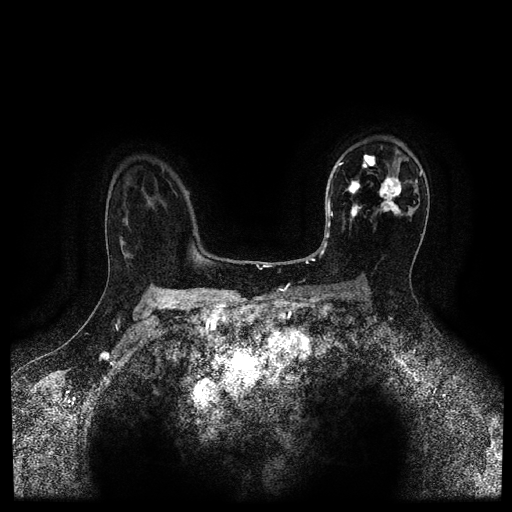
Breast MRI (dynamic contrast-enhanced, multi-phase), one axial slice; slice 70 of 116 in the series (ordered by position); dynamic contrast-enhanced series, time point 2 of 5 at this slice position (early post-contrast); 1.5 T; TE 2.7 ms, TR 5.4 ms; 2 mm slice thickness; 512 × 512 image matrix, field of view 340 × 340 mm. Female patient, age 50 years.
Outlined on this slice (semi-automatically segmented with operator editing):
- breast lesion (labelled 'tumour' in the annotation; benign lesions carry a separate 'benign' label): bounding box (x1, y1, x2, y2) in pixels: (344, 172, 409, 223)
- breast lesion (labelled 'tumour' in the annotation; benign lesions carry a separate 'benign' label): (362, 154, 377, 174)